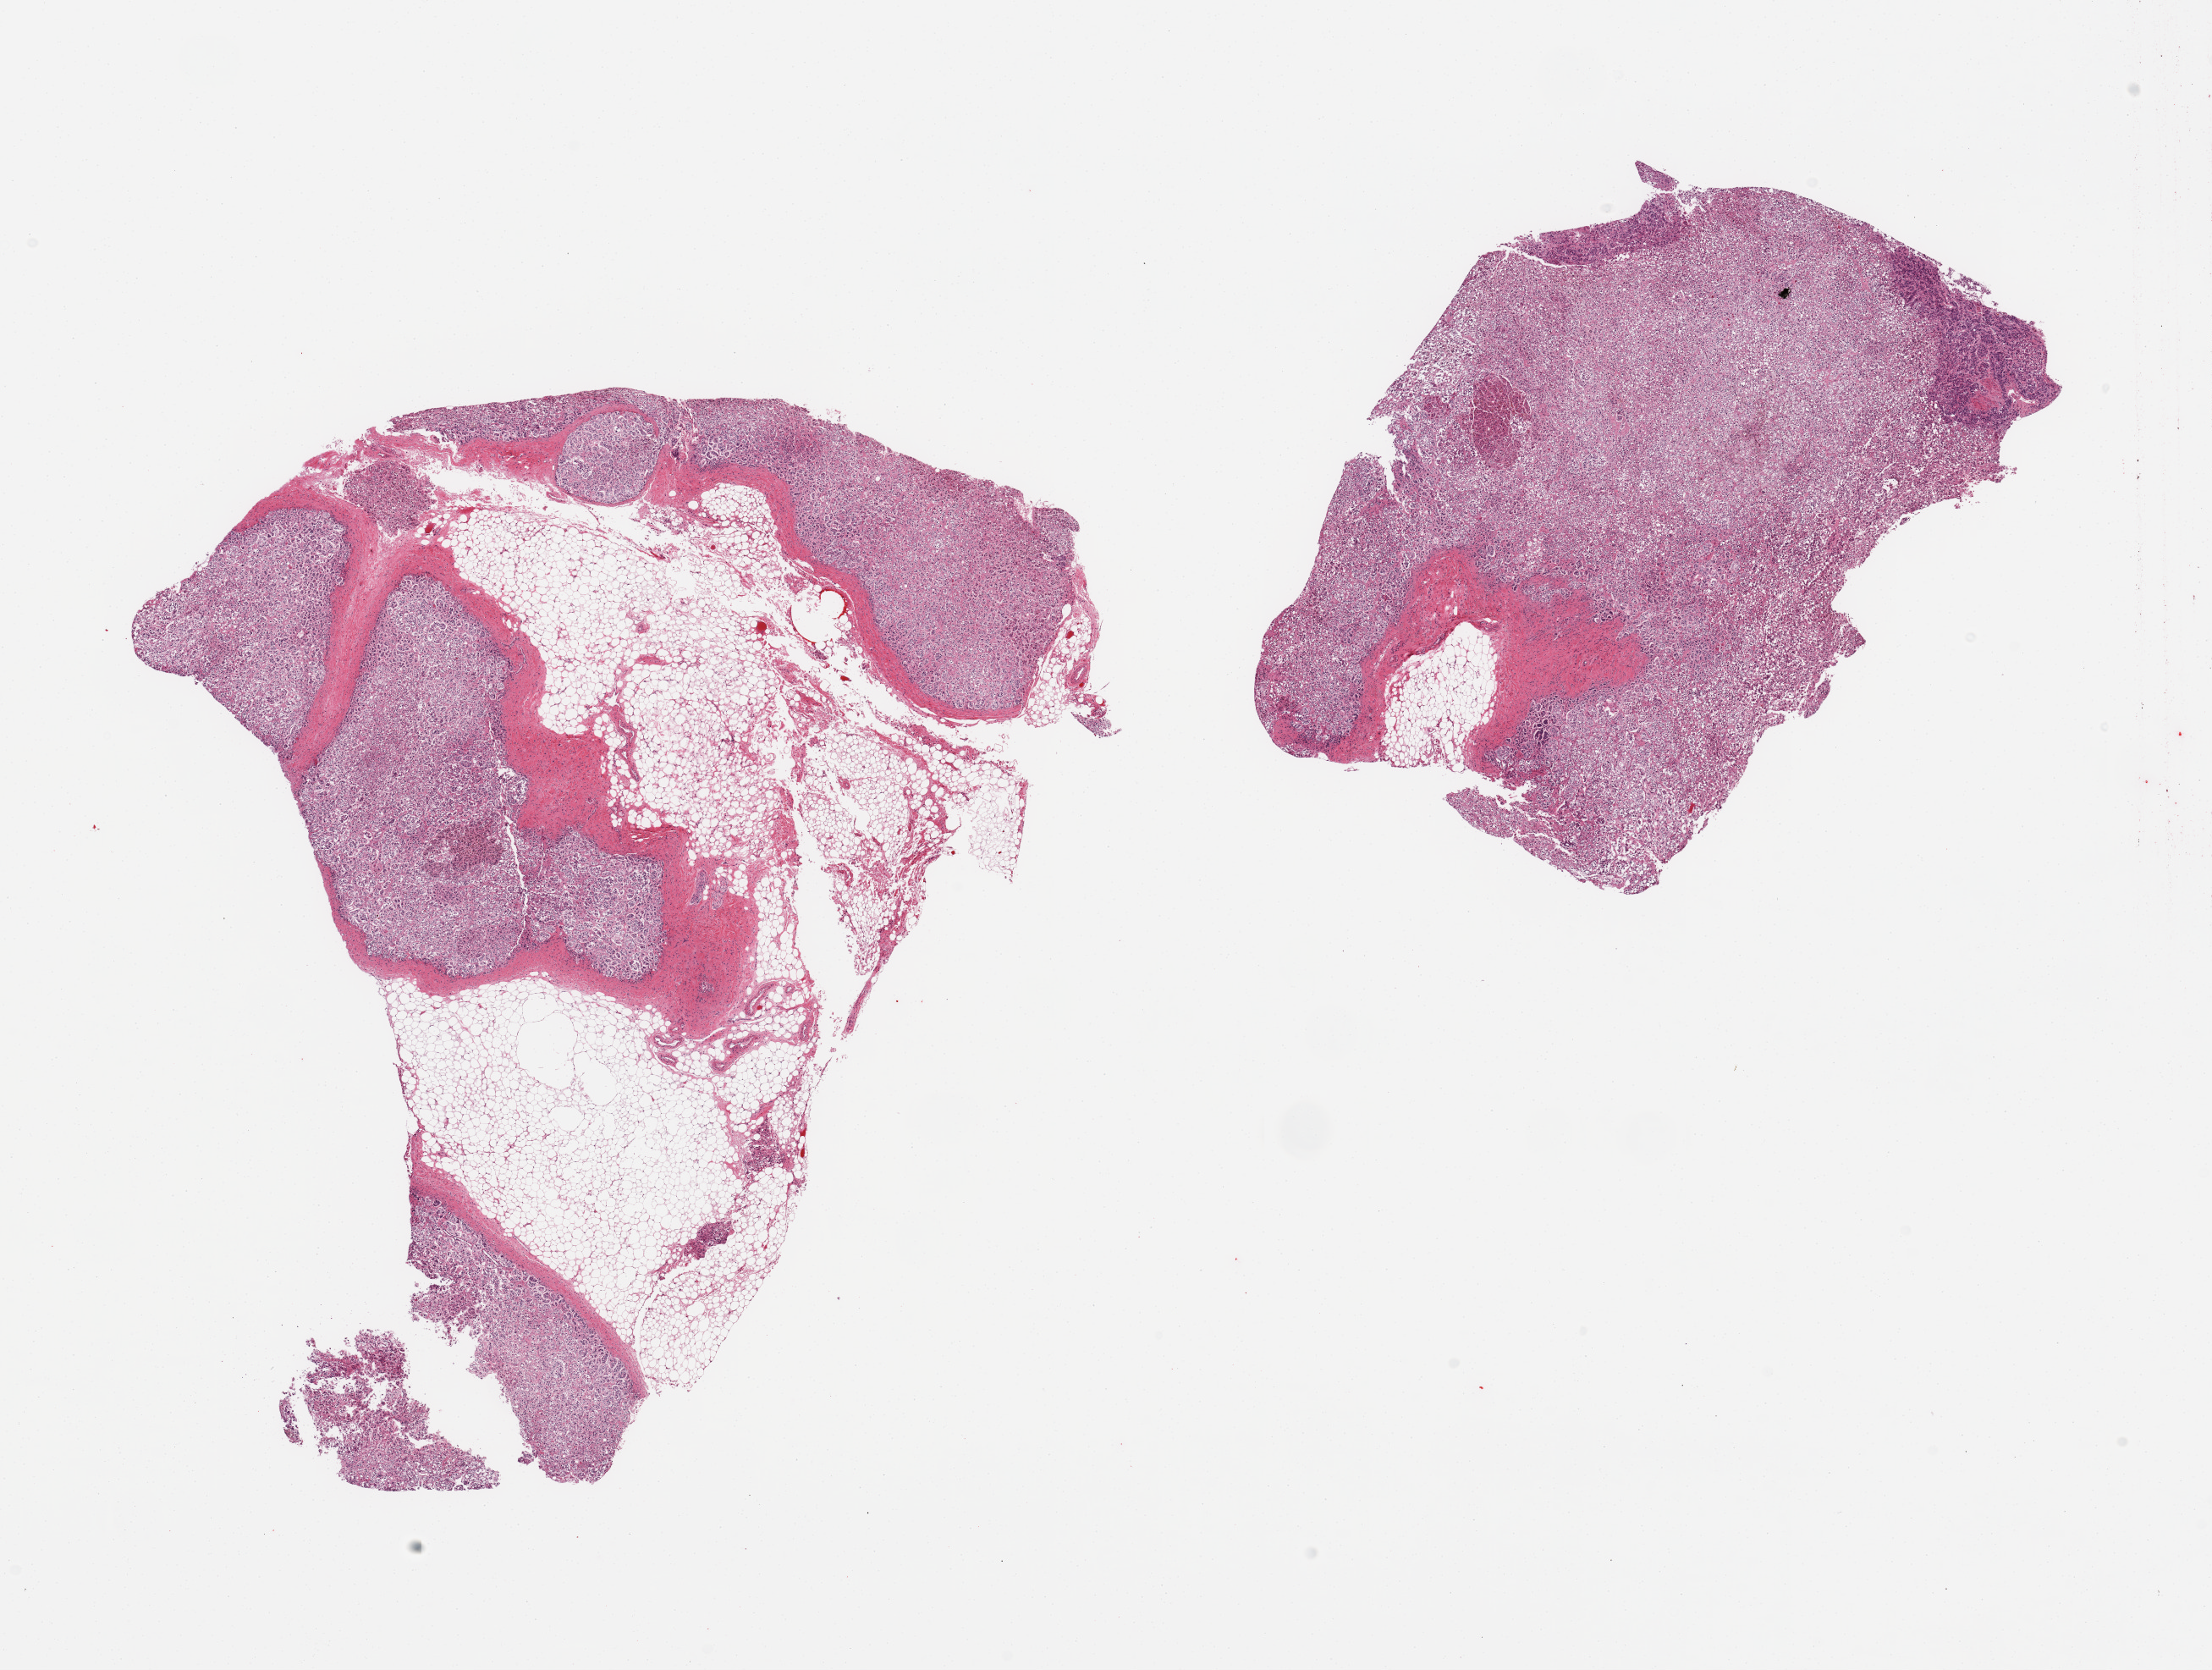
Whole-slide image, hematoxylin and eosin (H&E) stain, brightfield, shown as a low-resolution overview of the whole scanned area (about 20.7 x 15.6 mm, from a 20x scan). PAXgene-fixed, paraffin-embedded tissue. Sampled site (target tissue): adrenal gland. Donor tissue sample. Donor: male.
Pathologist's review note for this sample: 2 pieces; 50 & 10% fat.